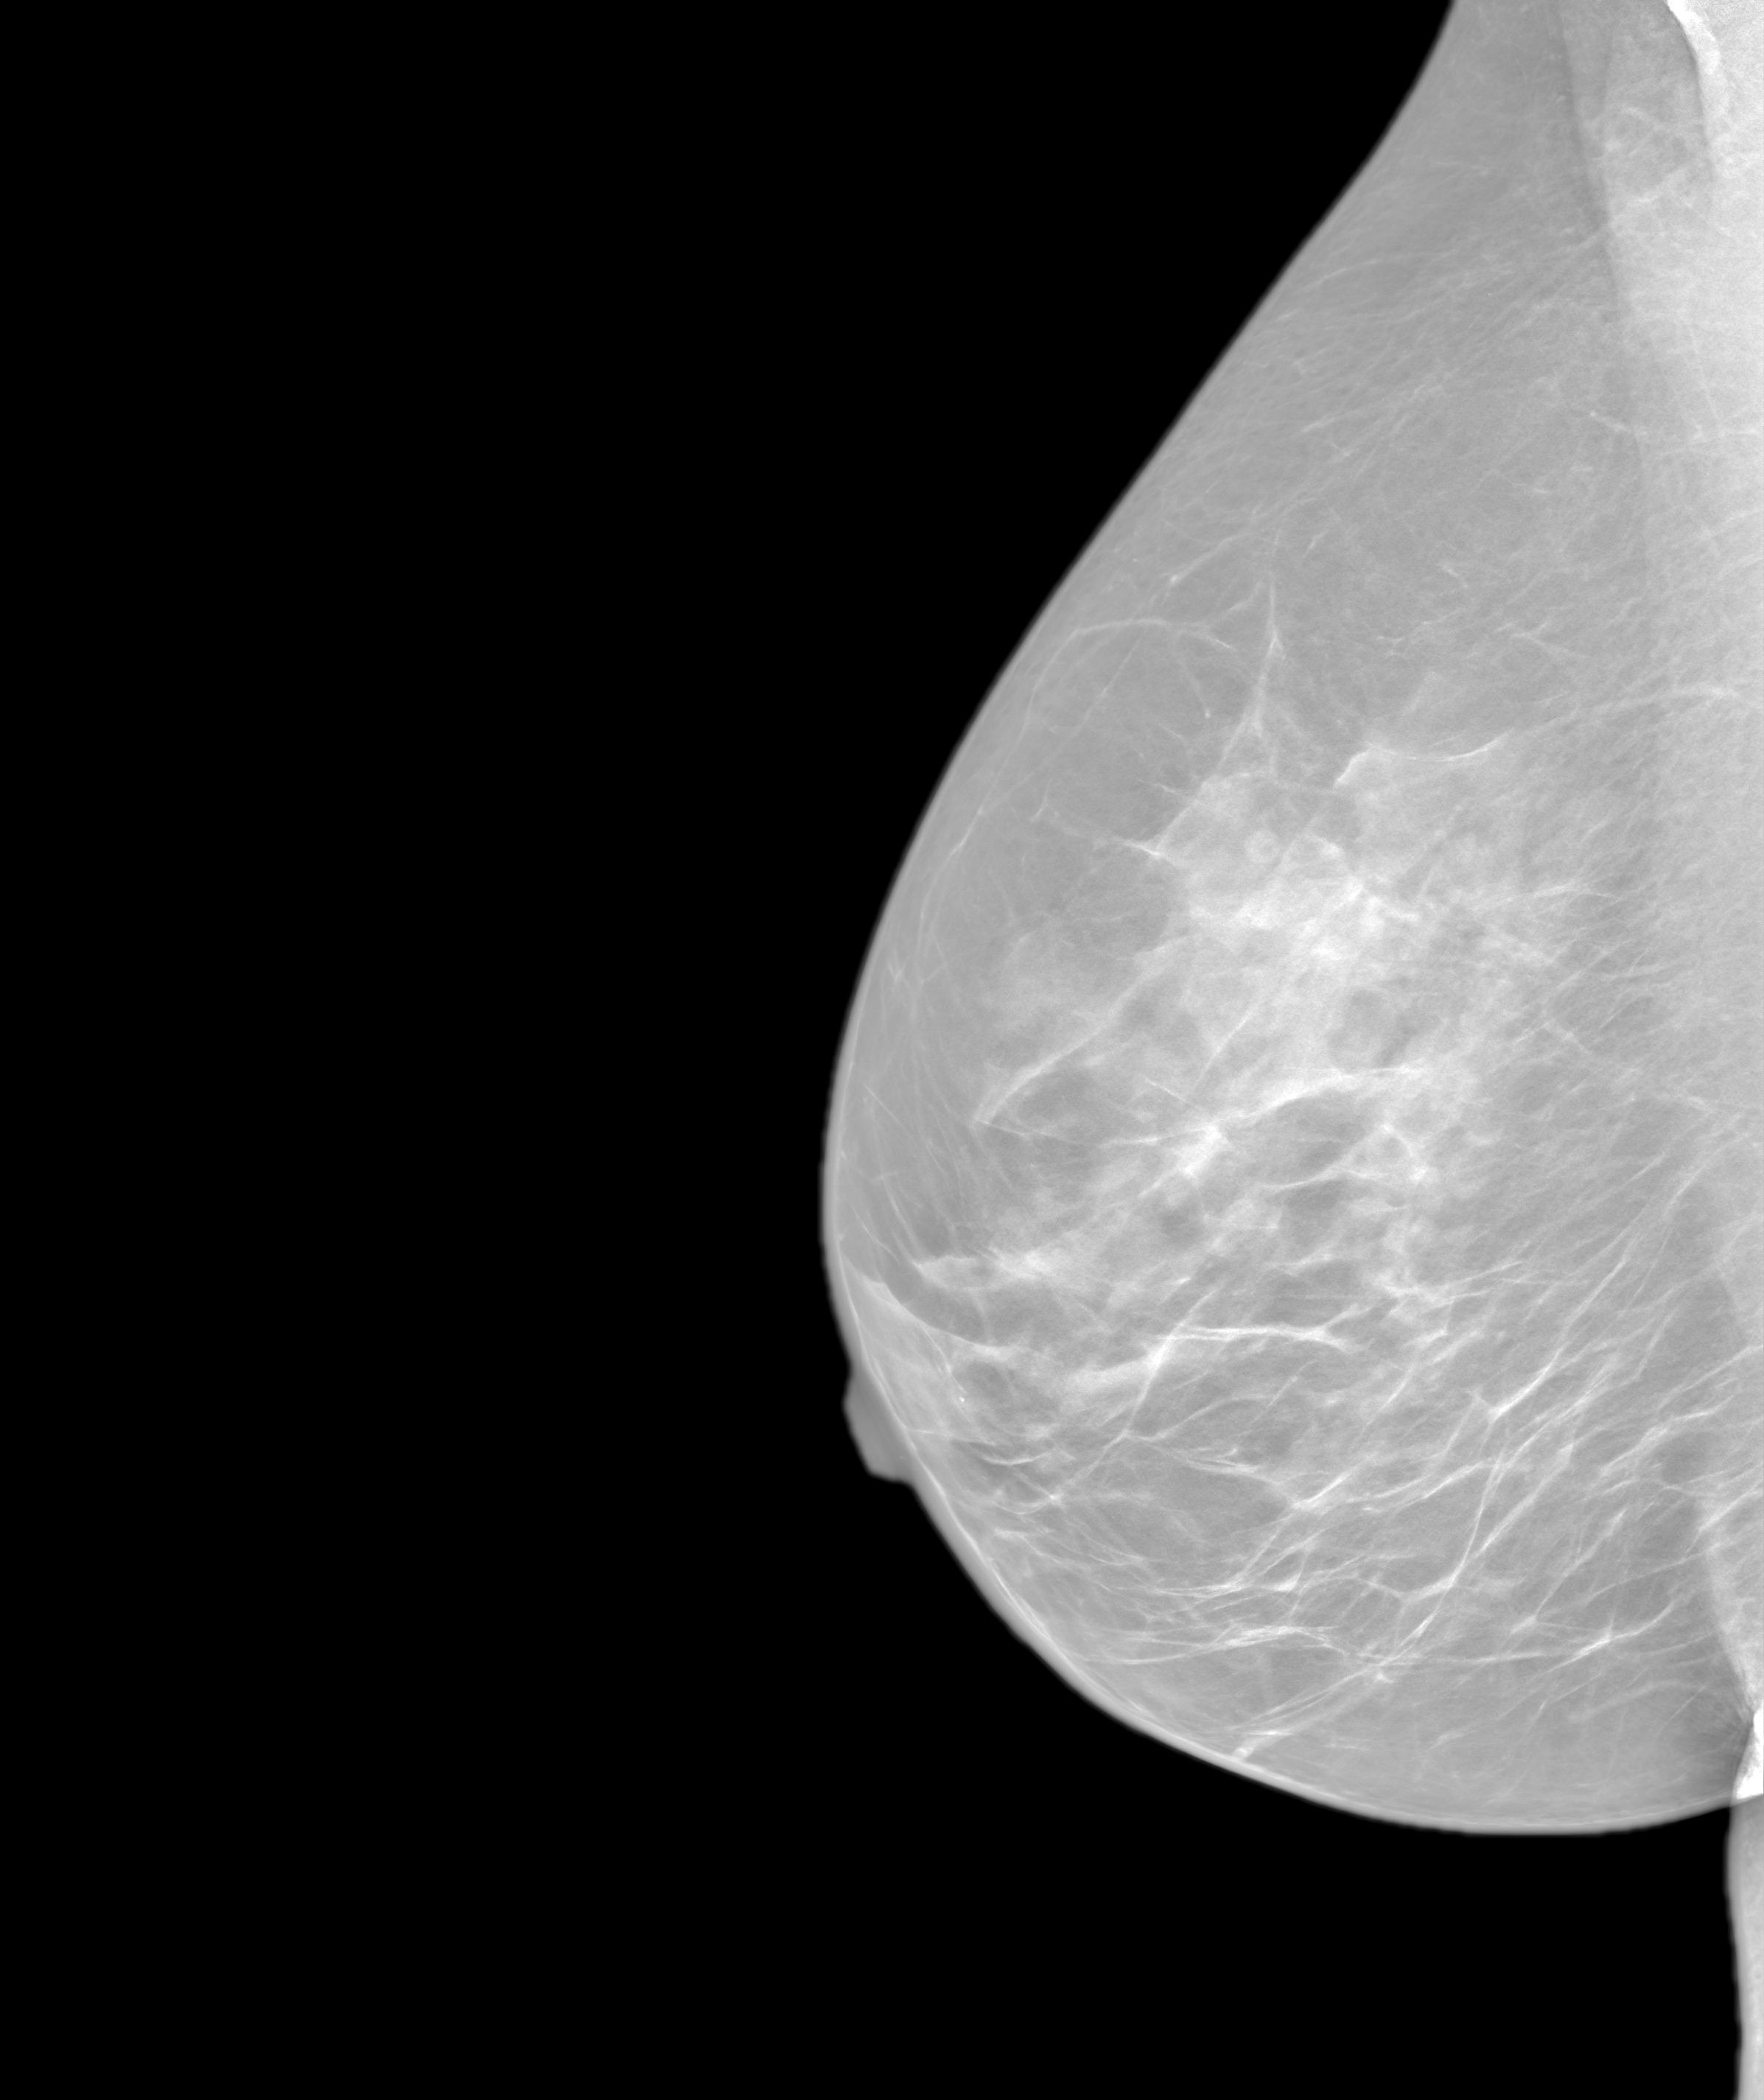
Screening examination. Patient aged 56 years (female).
Image type: synthesized 2-D view from tomosynthesis. Breast: right. Projection: MLO view.